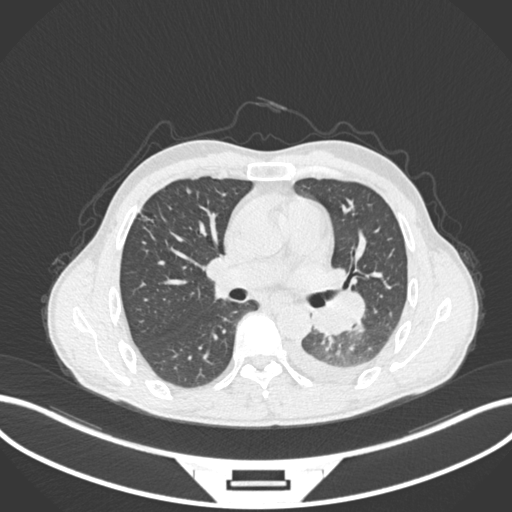
Chest CT, one axial slice; slice 137 of 222 in the series (ordered by position); lung window (W 1500 / L -600 HU); 1 mm slice thickness; 512 × 512 image matrix, field of view 400 × 400 mm. Male patient, age 47 years. Case-level facts recorded for this patient, not image findings: clinical TNM (as recorded): T3 N1 M1c; histopathological grade: G3.
Structures marked on this image (bounding box drawn by a radiologist):
- lung tumour (recorded histology: small cell carcinoma): box from (x=310, y=289) to (x=365, y=335) px